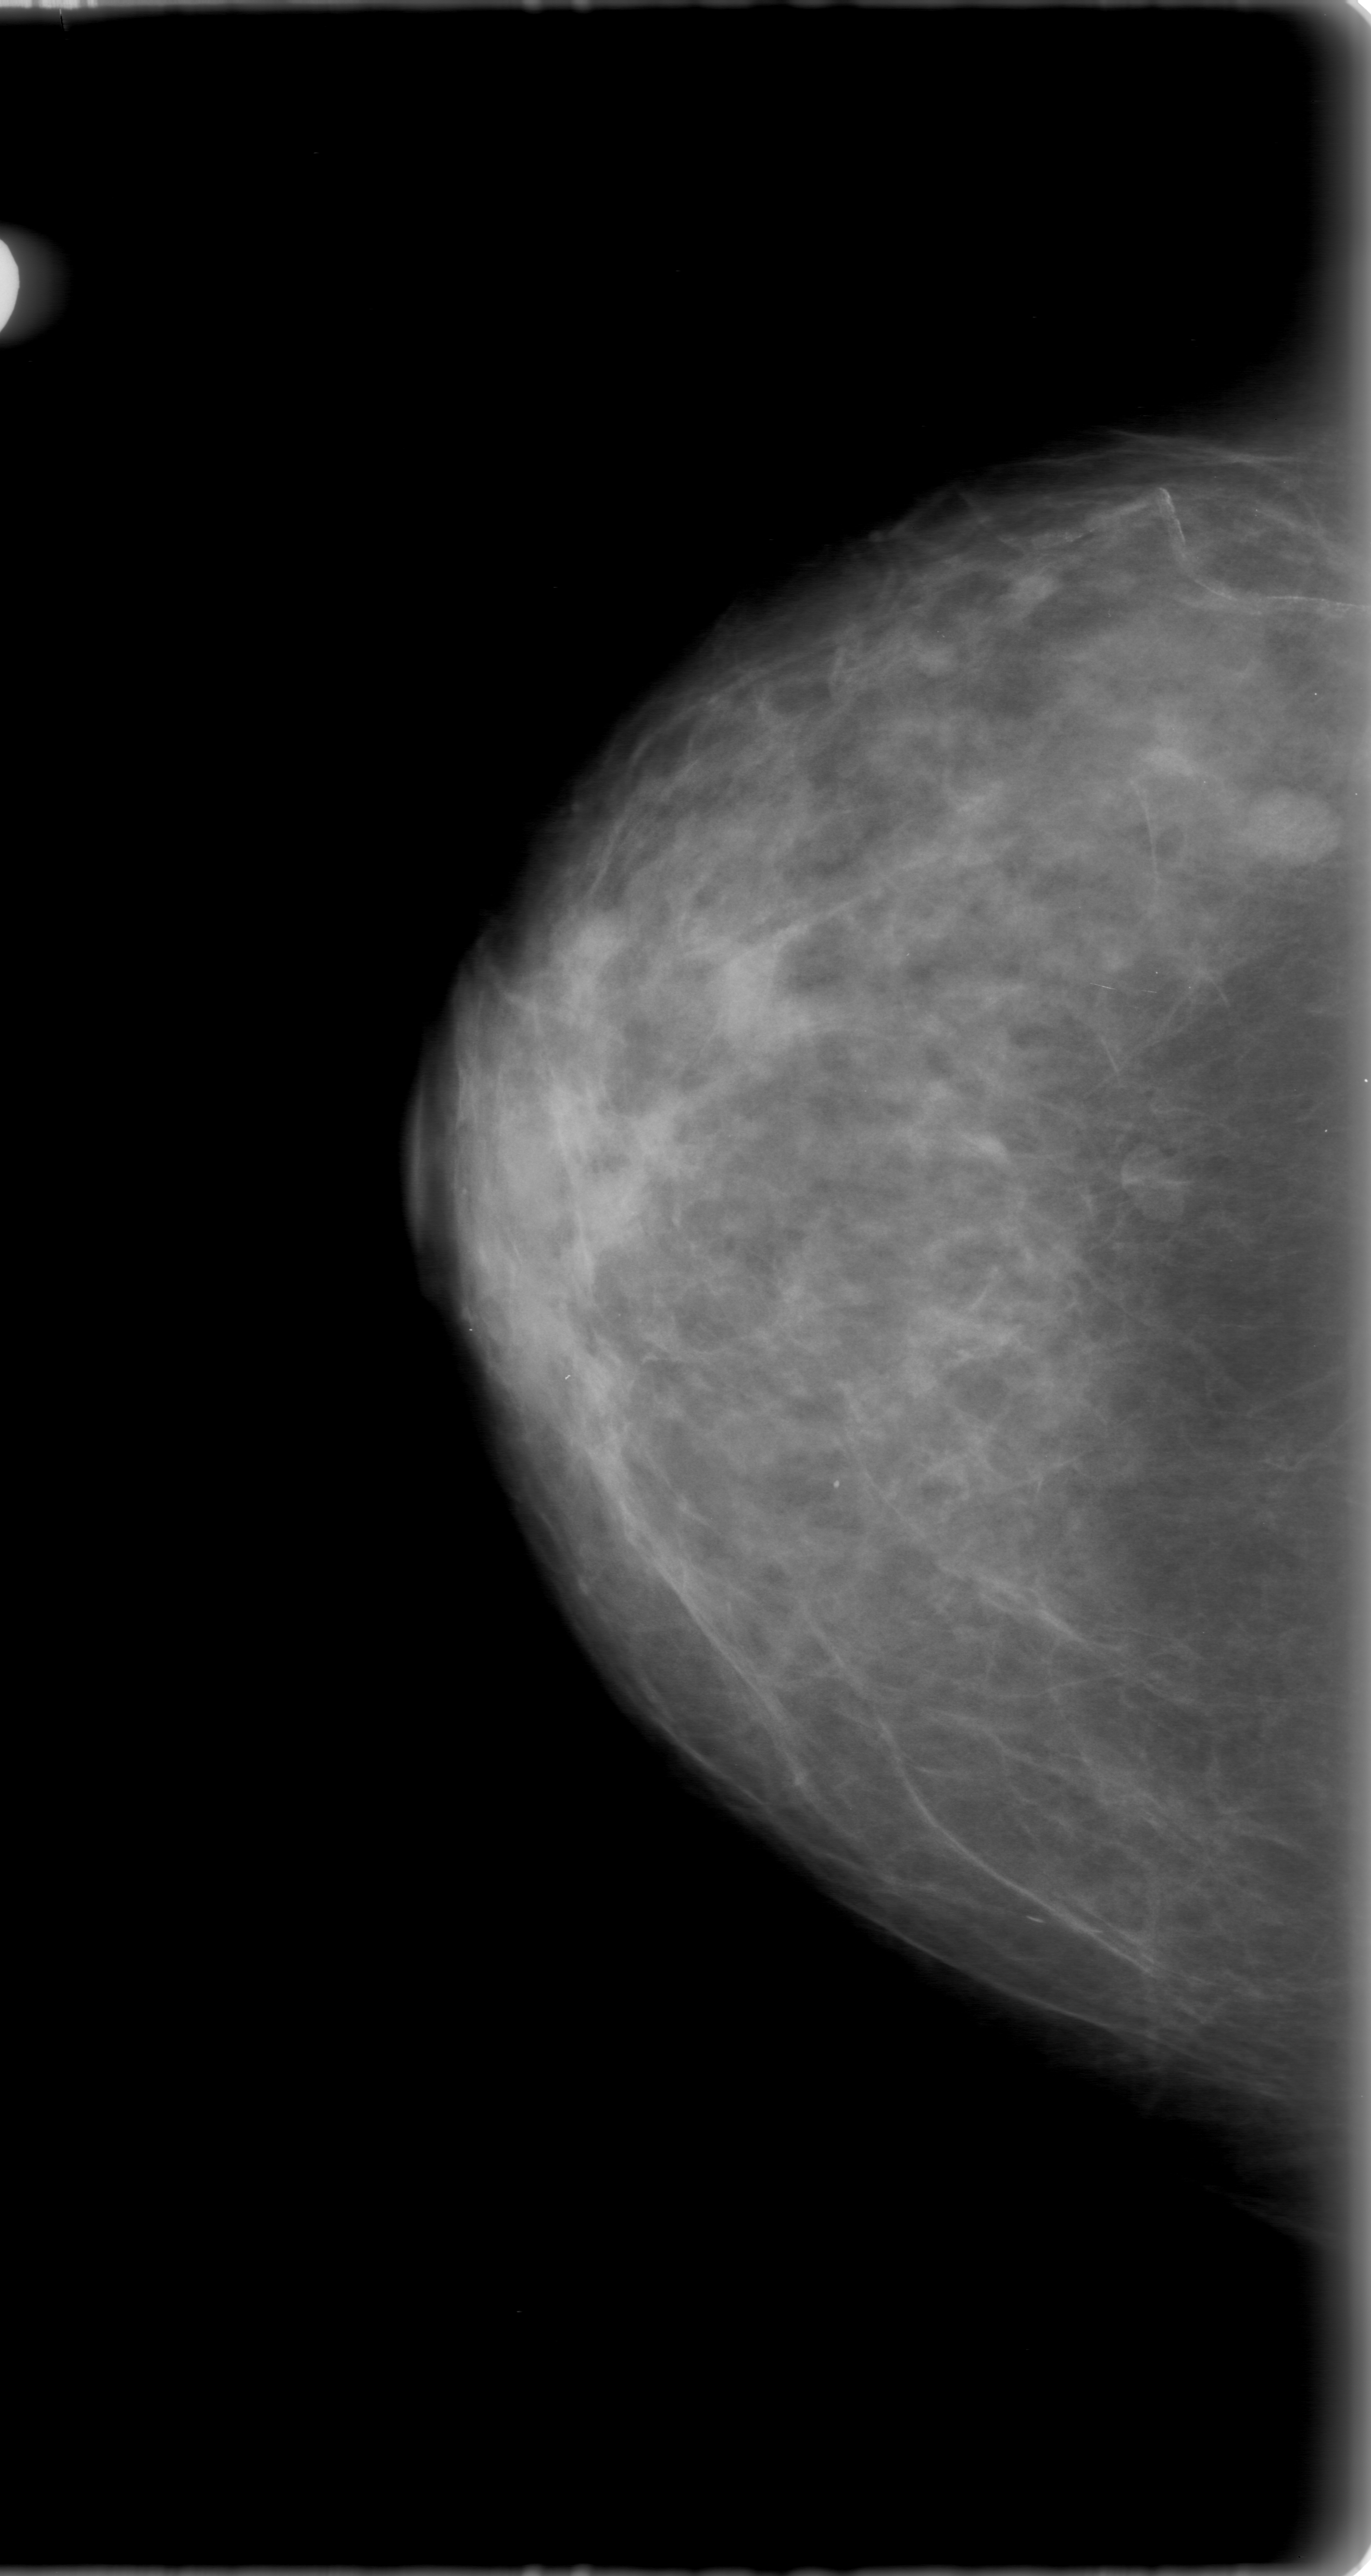
Digitized screen-film mammogram, right breast, craniocaudal (CC) view, BI-RADS breast density category 2 (scale 1–4).
Radiologist-marked abnormalities on this image: mass, shape oval, margins circumscribed; BI-RADS assessment category 0 (incomplete: needs additional imaging); pathology result (as recorded, not read from the image): benign.